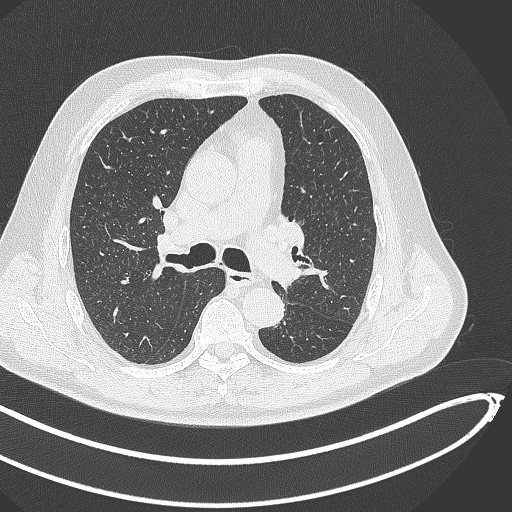
Chest CT, one axial slice; reconstruction kernel B70f; 120 kVp; lung window (W 1500 / L -600 HU); 1 mm slice thickness; 512 × 512 image matrix. Male patient, age 64 years. Case-level facts recorded for this patient, not image findings: clinical TNM (as recorded): T1c N0 M0; histopathological grade: G2.
Outlined on this slice (bounding box drawn by a radiologist):
- lung tumour (recorded histology: squamous cell carcinoma): bounding box (x1, y1, x2, y2) in pixels: (274, 265, 305, 290)